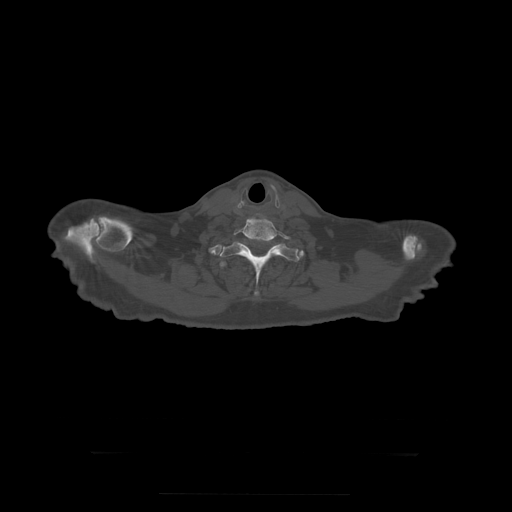
CT including the spine, one axial slice; position 292 of 397 along the scan axis; reconstruction kernel STANDARD; 120 kVp; bone window (W 1800 / L 400 HU); 512 × 512 image matrix. Patient age 73 years. Case-level facts recorded for this patient, not image findings: primary cancer: prostate.
Annotated regions visible in this slice (semi-automatic segmentation, software-assisted and operator-edited):
- T1 vertebra: bounding box <218,241,300,296> (left, top, right, bottom; pixels)
- T2 vertebra: <220,261,227,268>